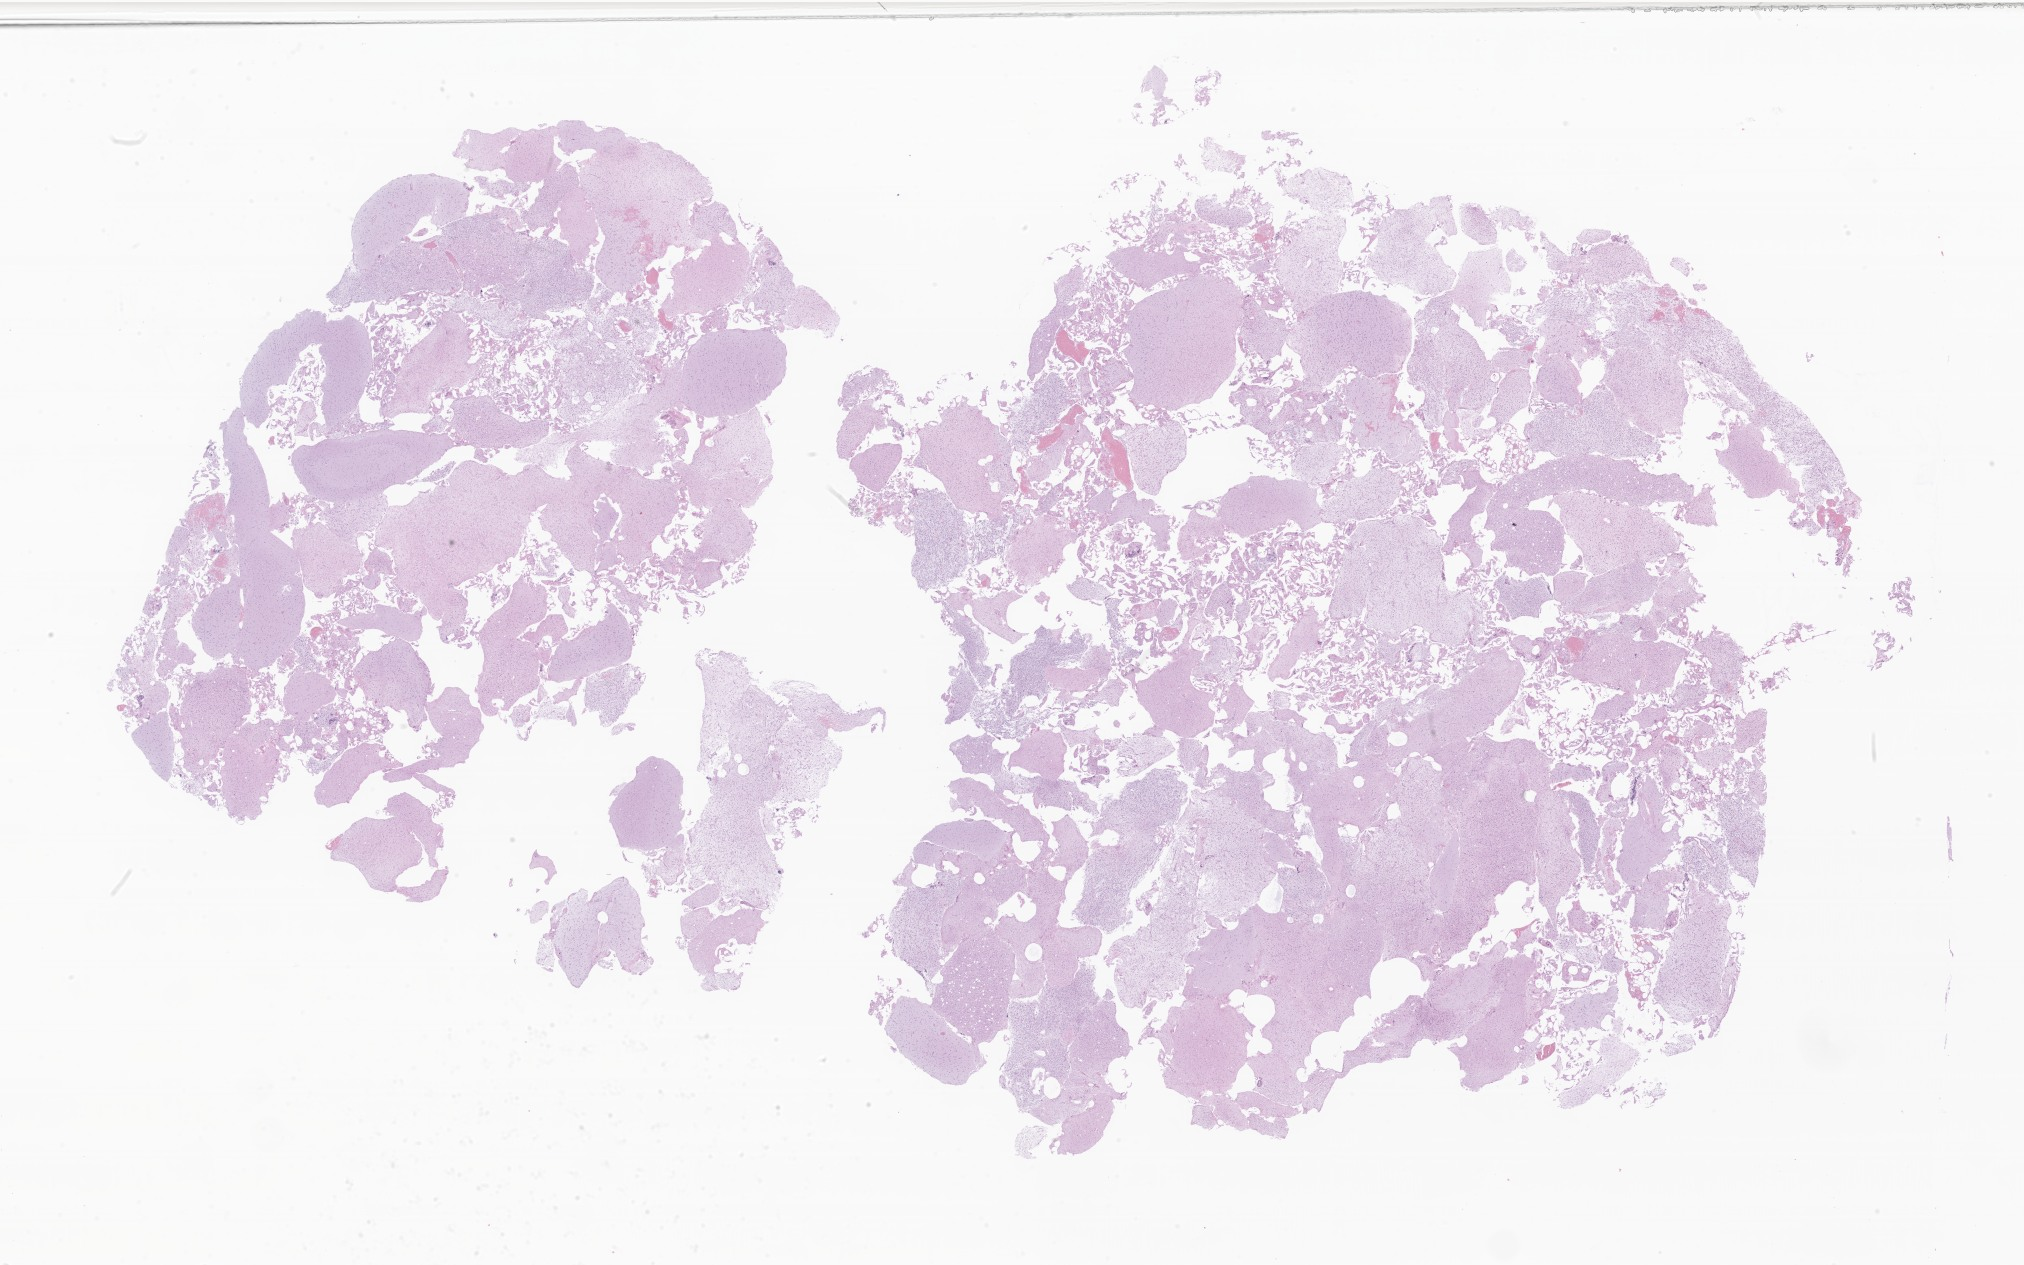
Digitized hematoxylin and eosin (H&E)-stained section of tumor tissue from the brain, whole scanned area (about 34.1 x 21.3 mm) shown as a low-resolution overview, formalin-fixed, paraffin-embedded (FFPE) tissue. Male patient, age 240 months (20 years).
Diagnosis (ICD-O-3 morphology term): Astrocytoma, NOS.